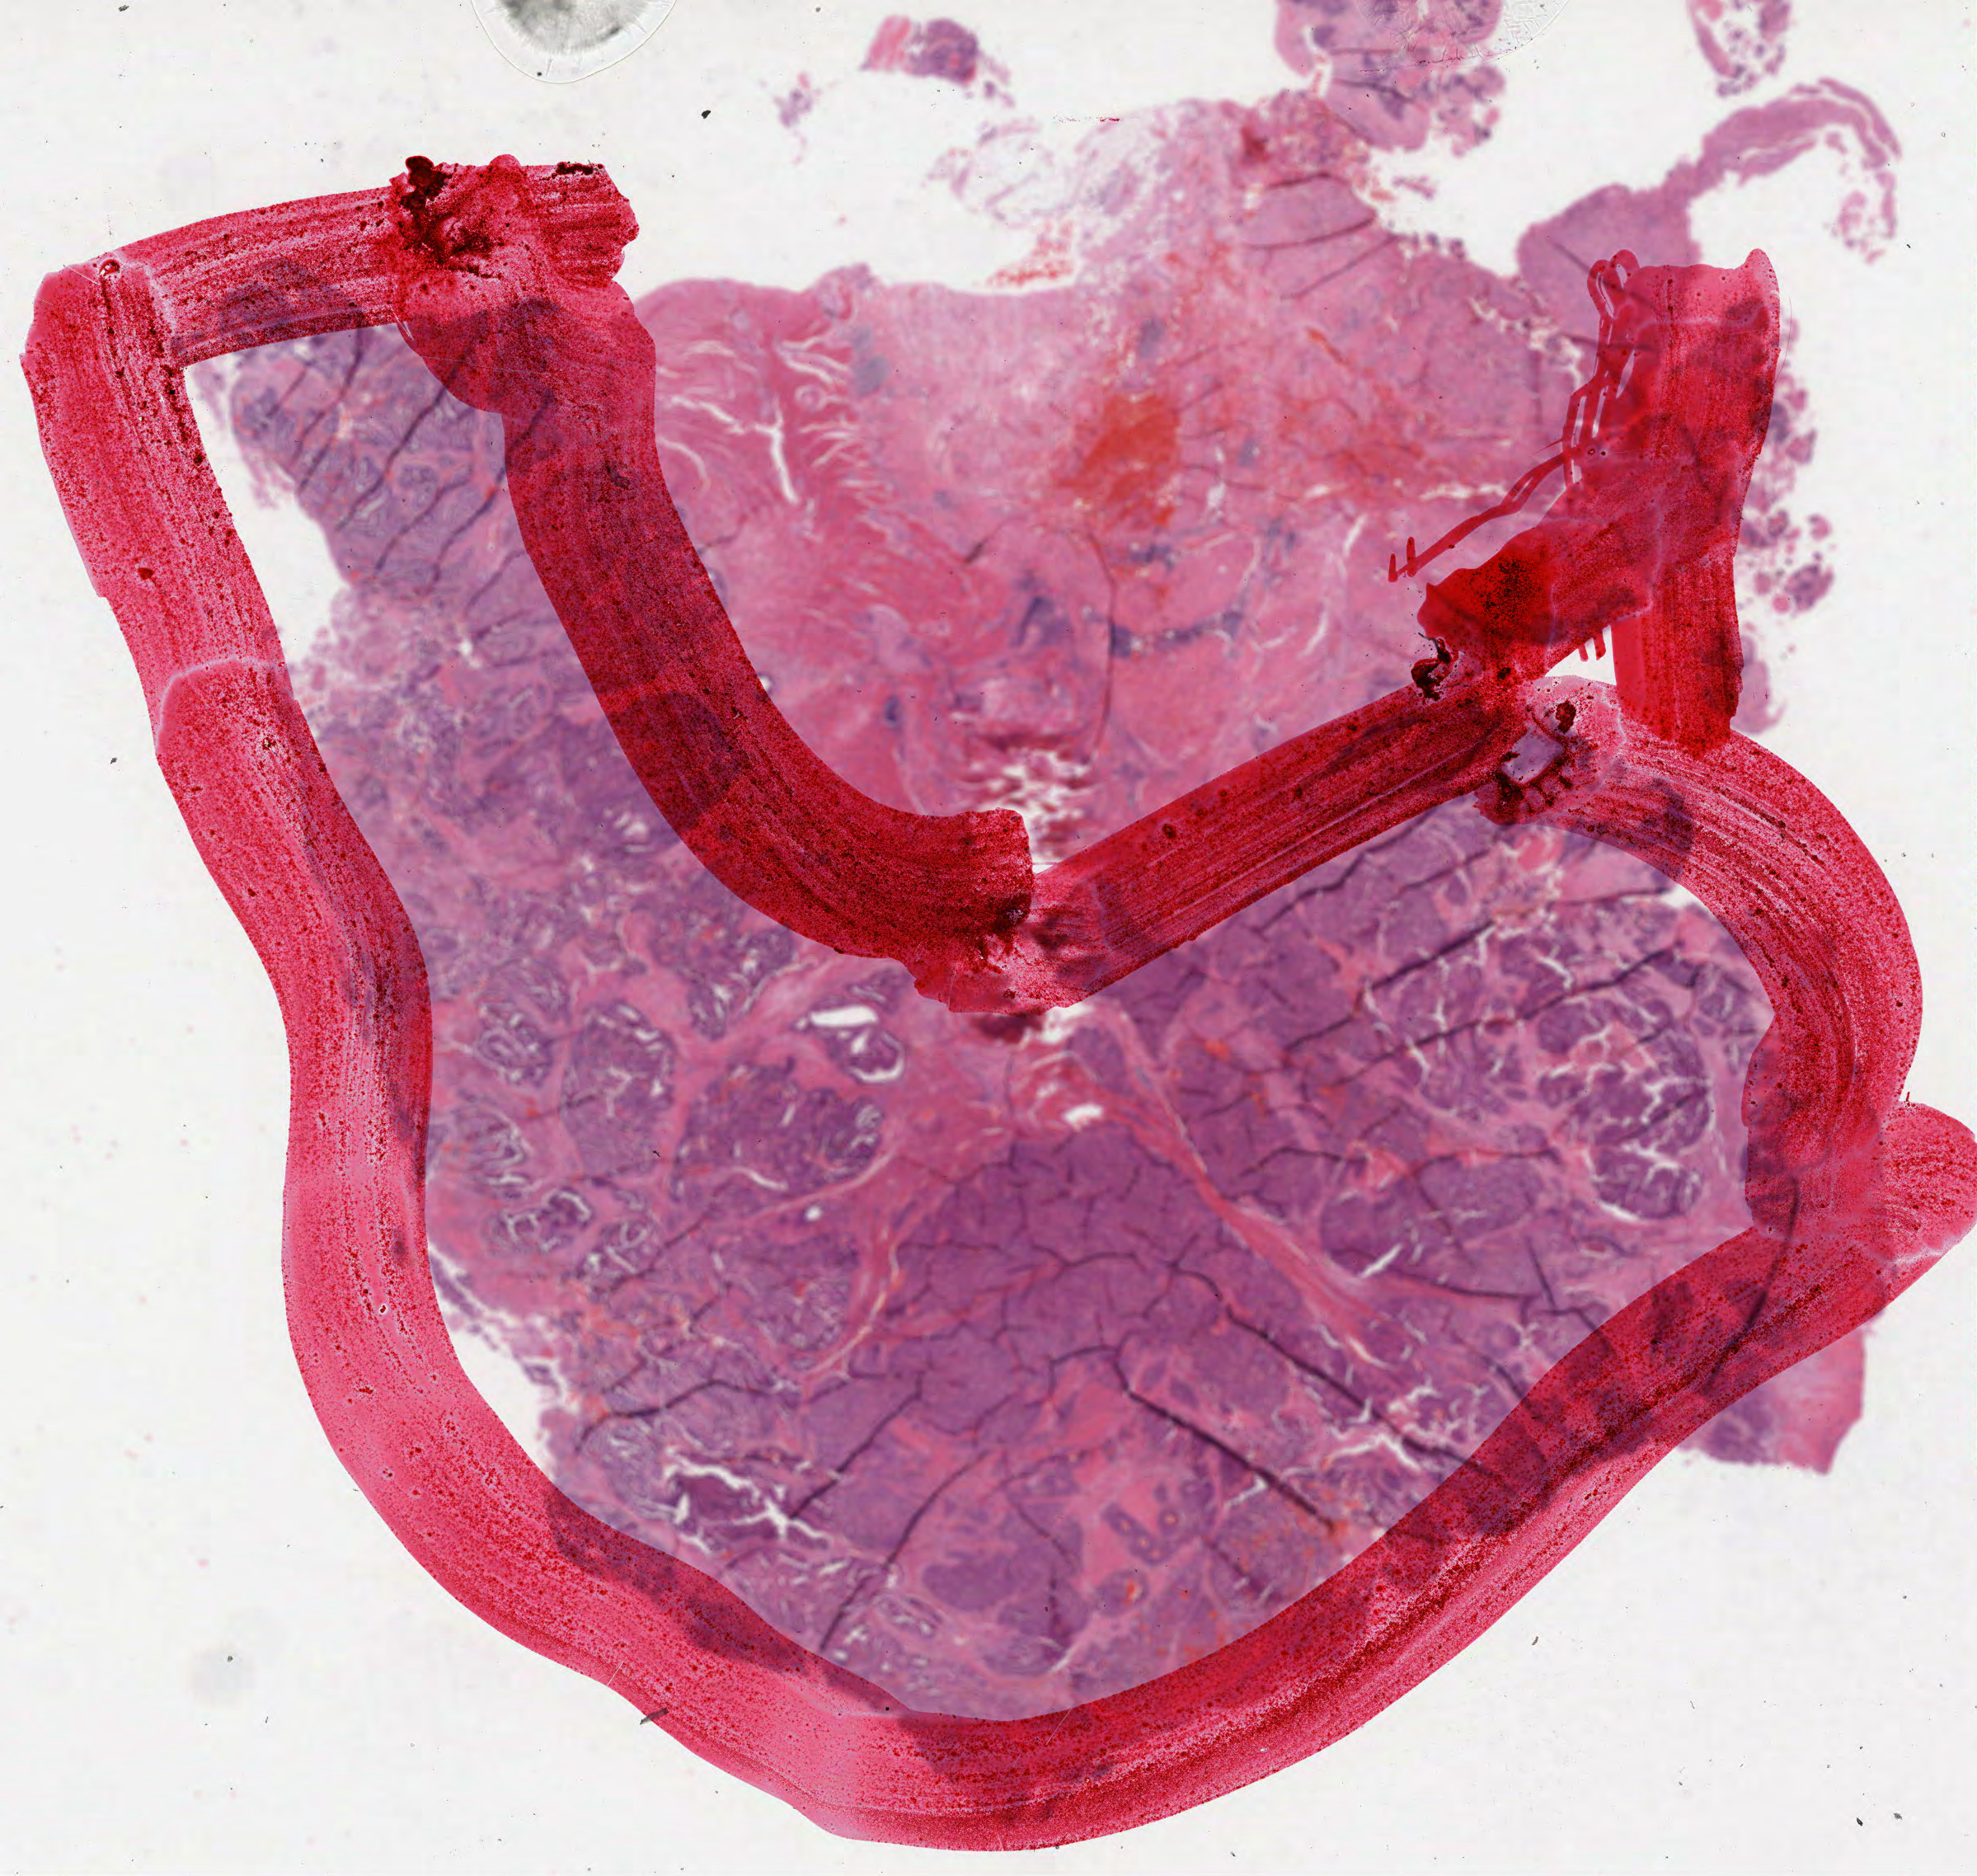
Digitized H&E-stained tissue section (whole slide) — a low-resolution overview of the entire scanned area, about 19.3 x 18.3 mm (slide scanned at 40x), FFPE section, primary tumour sample from the rectum. Patient: male, age at initial diagnosis 57 years.
TNM: T3 N0 M0. AJCC pathologic stage: IIA. Pathologic diagnosis: Adenocarcinoma, NOS.